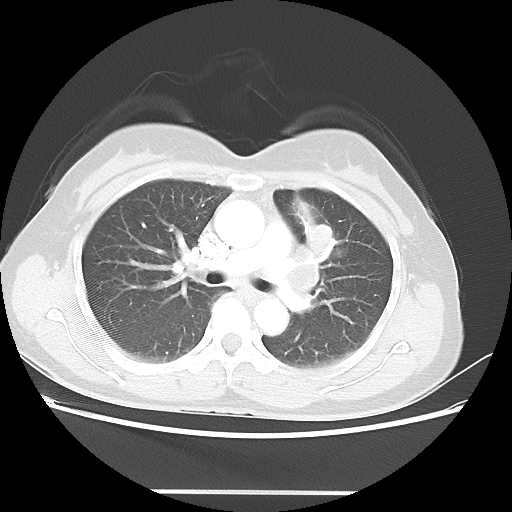
Chest CT, one axial slice. Position 28 of 46 along the scan axis. 100 kVp. Lung window (W 1500 / L -600 HU). 5 mm slice thickness. 512 × 512 image matrix, field of view 360 × 360 mm. Female patient, age 50 years. From the clinical record (not read from this slice): clinical TNM (as recorded): T1c N1 M0; histopathological grade: G3.
Outlined on this slice (bounding box drawn by a radiologist):
- lung tumour (recorded histology: adenocarcinoma): bounding box <289,198,340,260> (left, top, right, bottom; pixels)